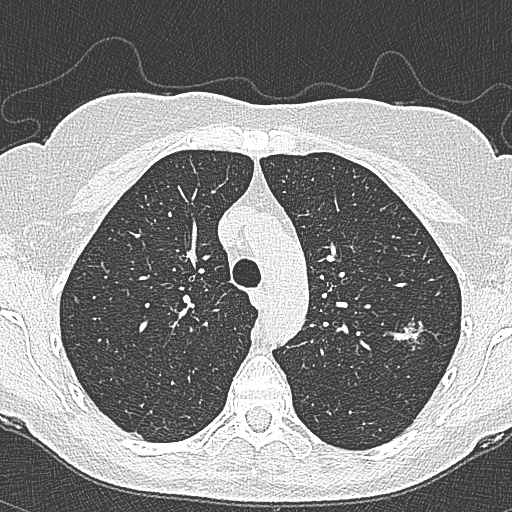
Low-dose screening chest CT, axial slice. Second annual screen. Lung window (W 1500 / L -600 HU). 1 mm slice thickness. 512 × 512 image matrix, field of view 298 × 298 mm. Female participant, aged 65 years at enrolment.
Expert reader's lesion annotation, bounding box [x1, y1, x2, y2] px = [393, 310, 439, 357]. The screening reader recorded 4 non-calcified nodules or masses ≥4 mm on this exam (left upper lobe, left upper lobe, left upper lobe, right lower lobe); which of them this box marks is not recorded. Later outcome: lung cancer diagnosed 54 days after this screen — bronchiolo-alveolar carcinoma, non-mucinous, left upper lobe, stage IA (AJCC 6th edition), 10 mm at pathology.